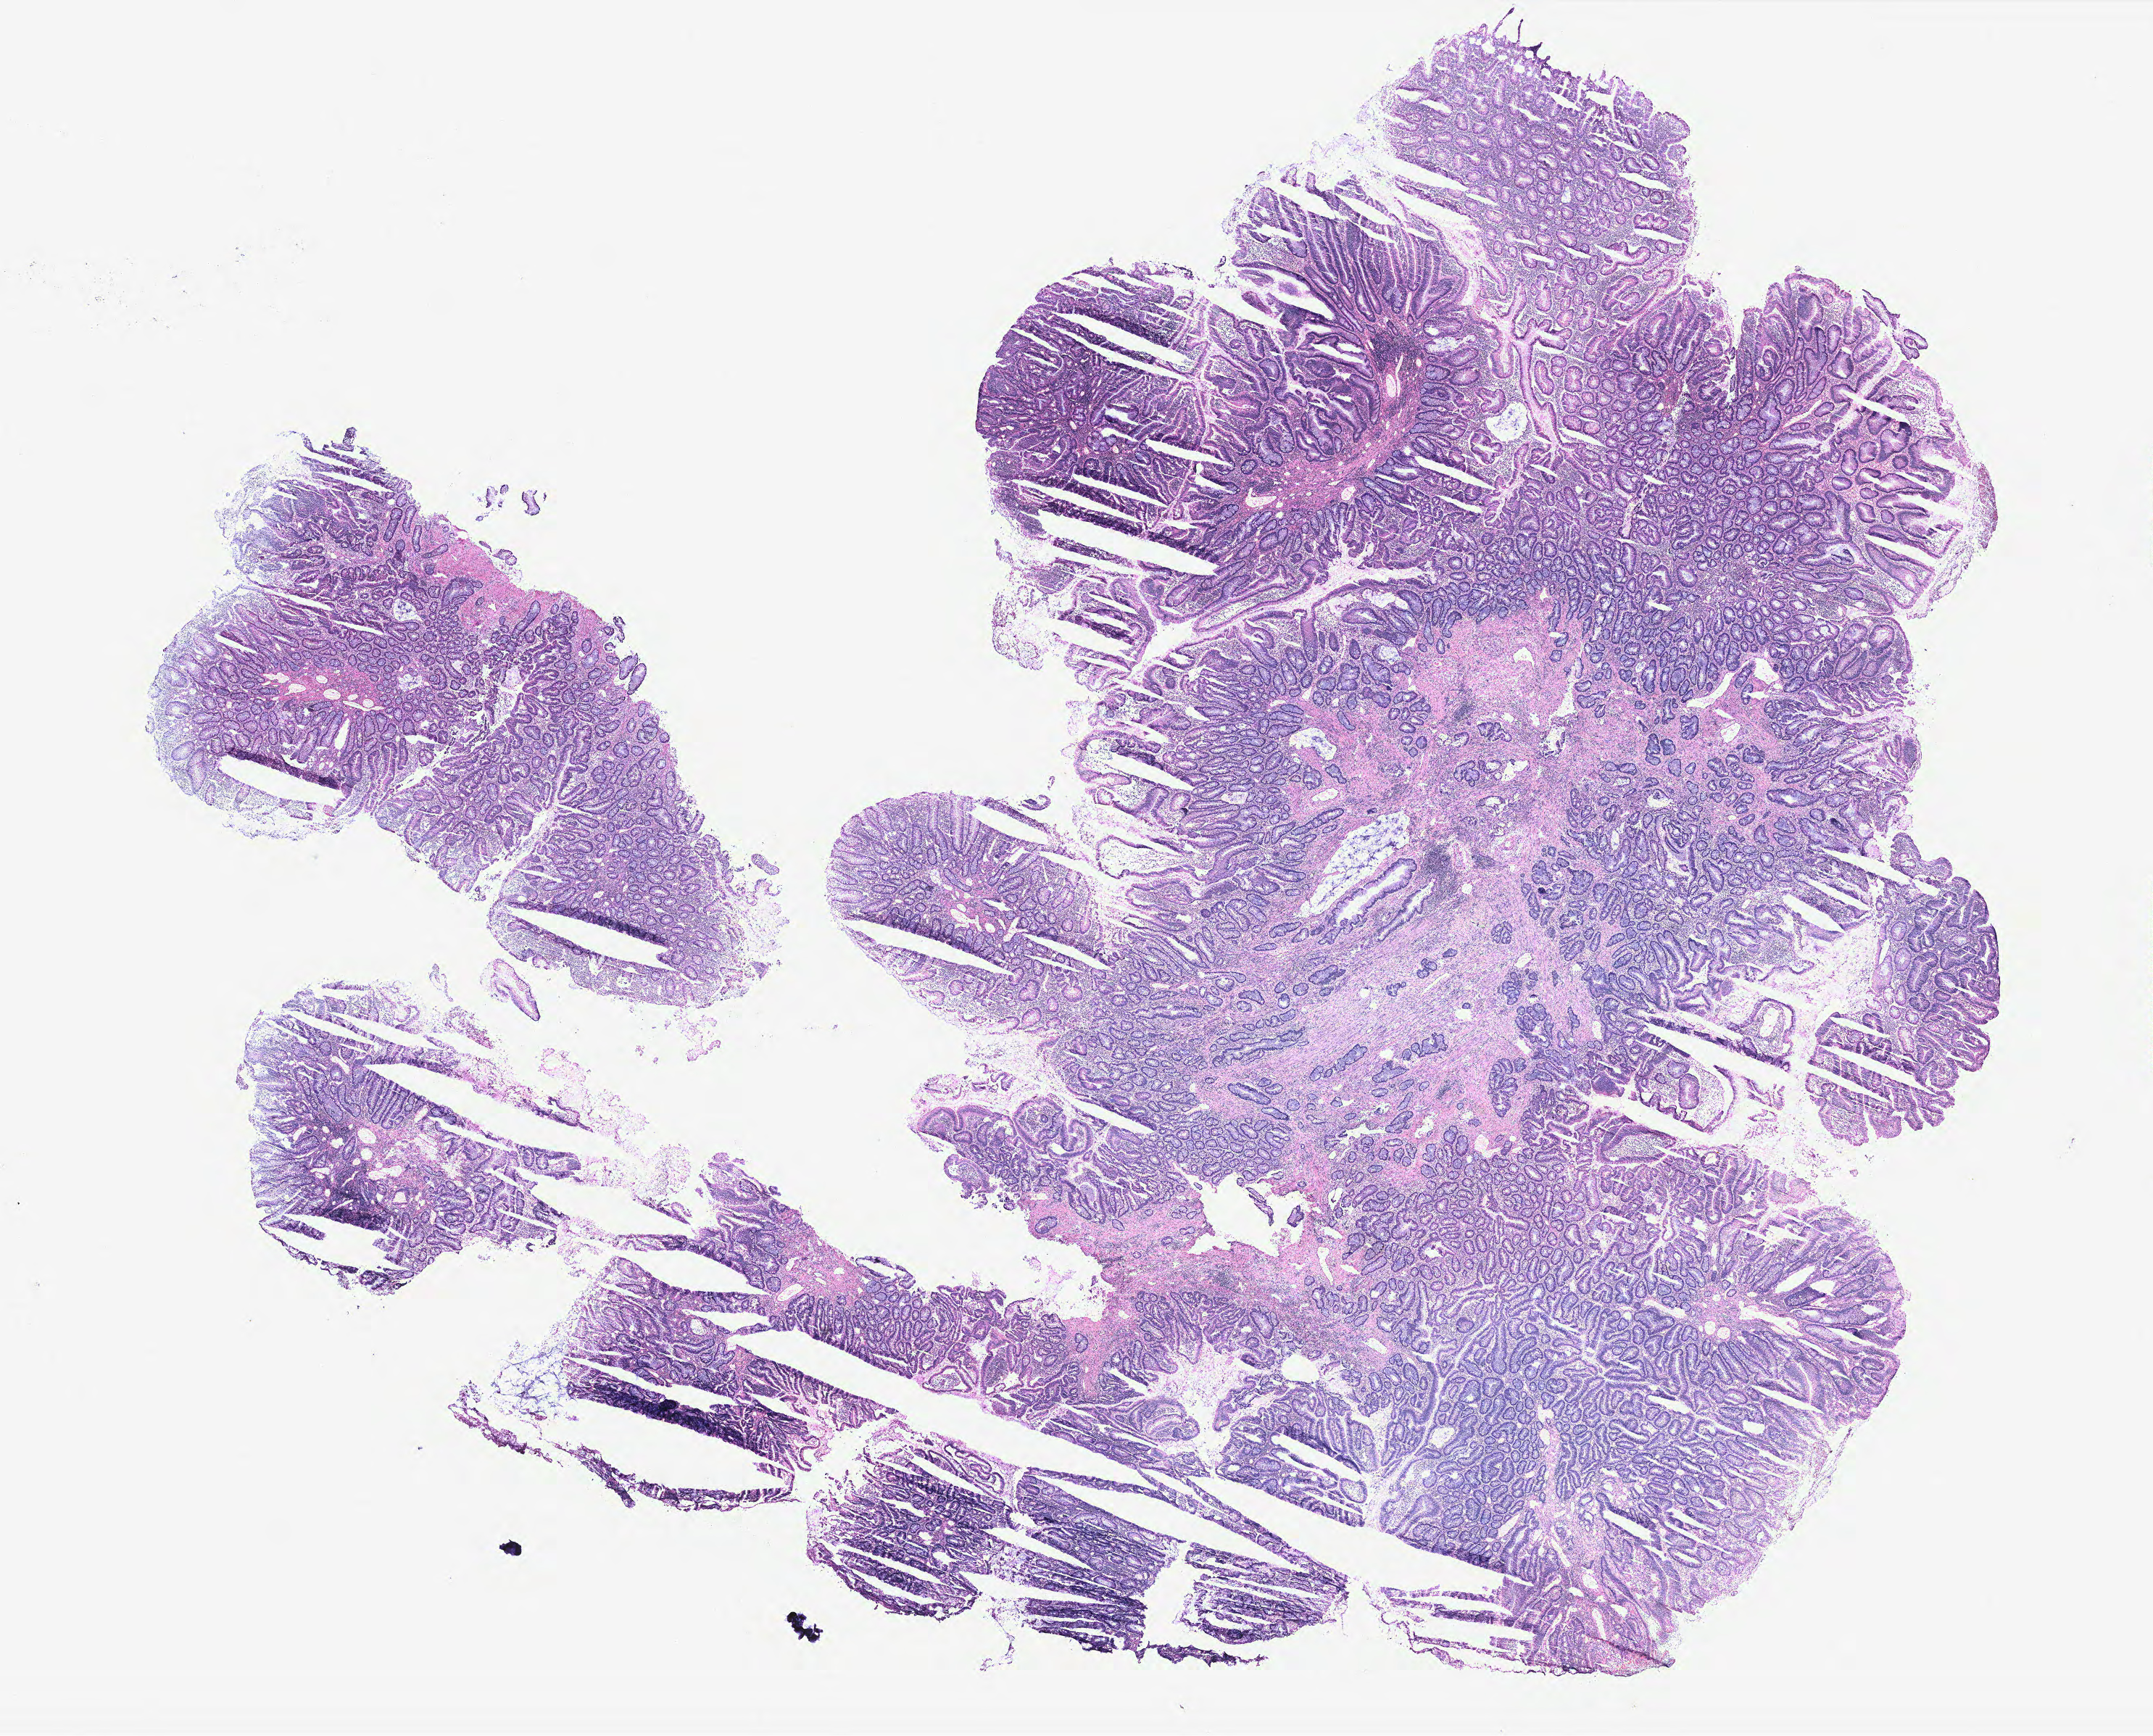
Hematoxylin and eosin (H&E) stained whole-slide image — whole scanned area (about 23.8 x 19.2 mm, slide scanned at 40x) shown as a low-resolution overview, colon, tissue type not recorded.
Patient diagnosis (cohort enrolment): colon cancer (colon).